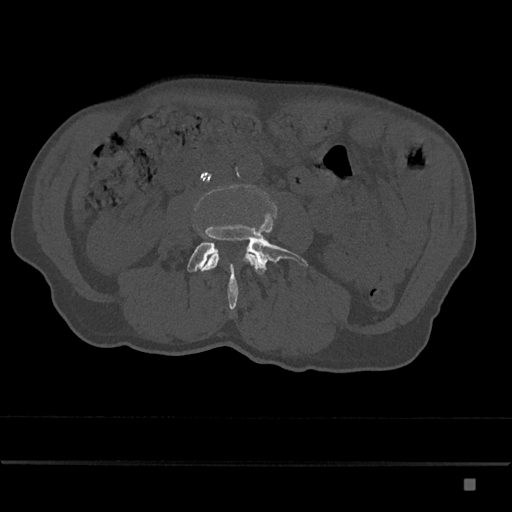
CT including the spine, one axial slice; position 362 of 797 along the scan axis; bone window (W 1800 / L 400 HU); 512 × 512 image matrix. Male patient, age 72 years. Case-level facts recorded for this patient, not image findings: primary cancer: prostate.
Structures marked on this image (semi-automatically segmented with operator editing):
- L3 vertebra: bounding box [x1, y1, x2, y2] px = [202, 253, 259, 271]
- L4 vertebra: [187, 213, 308, 309]